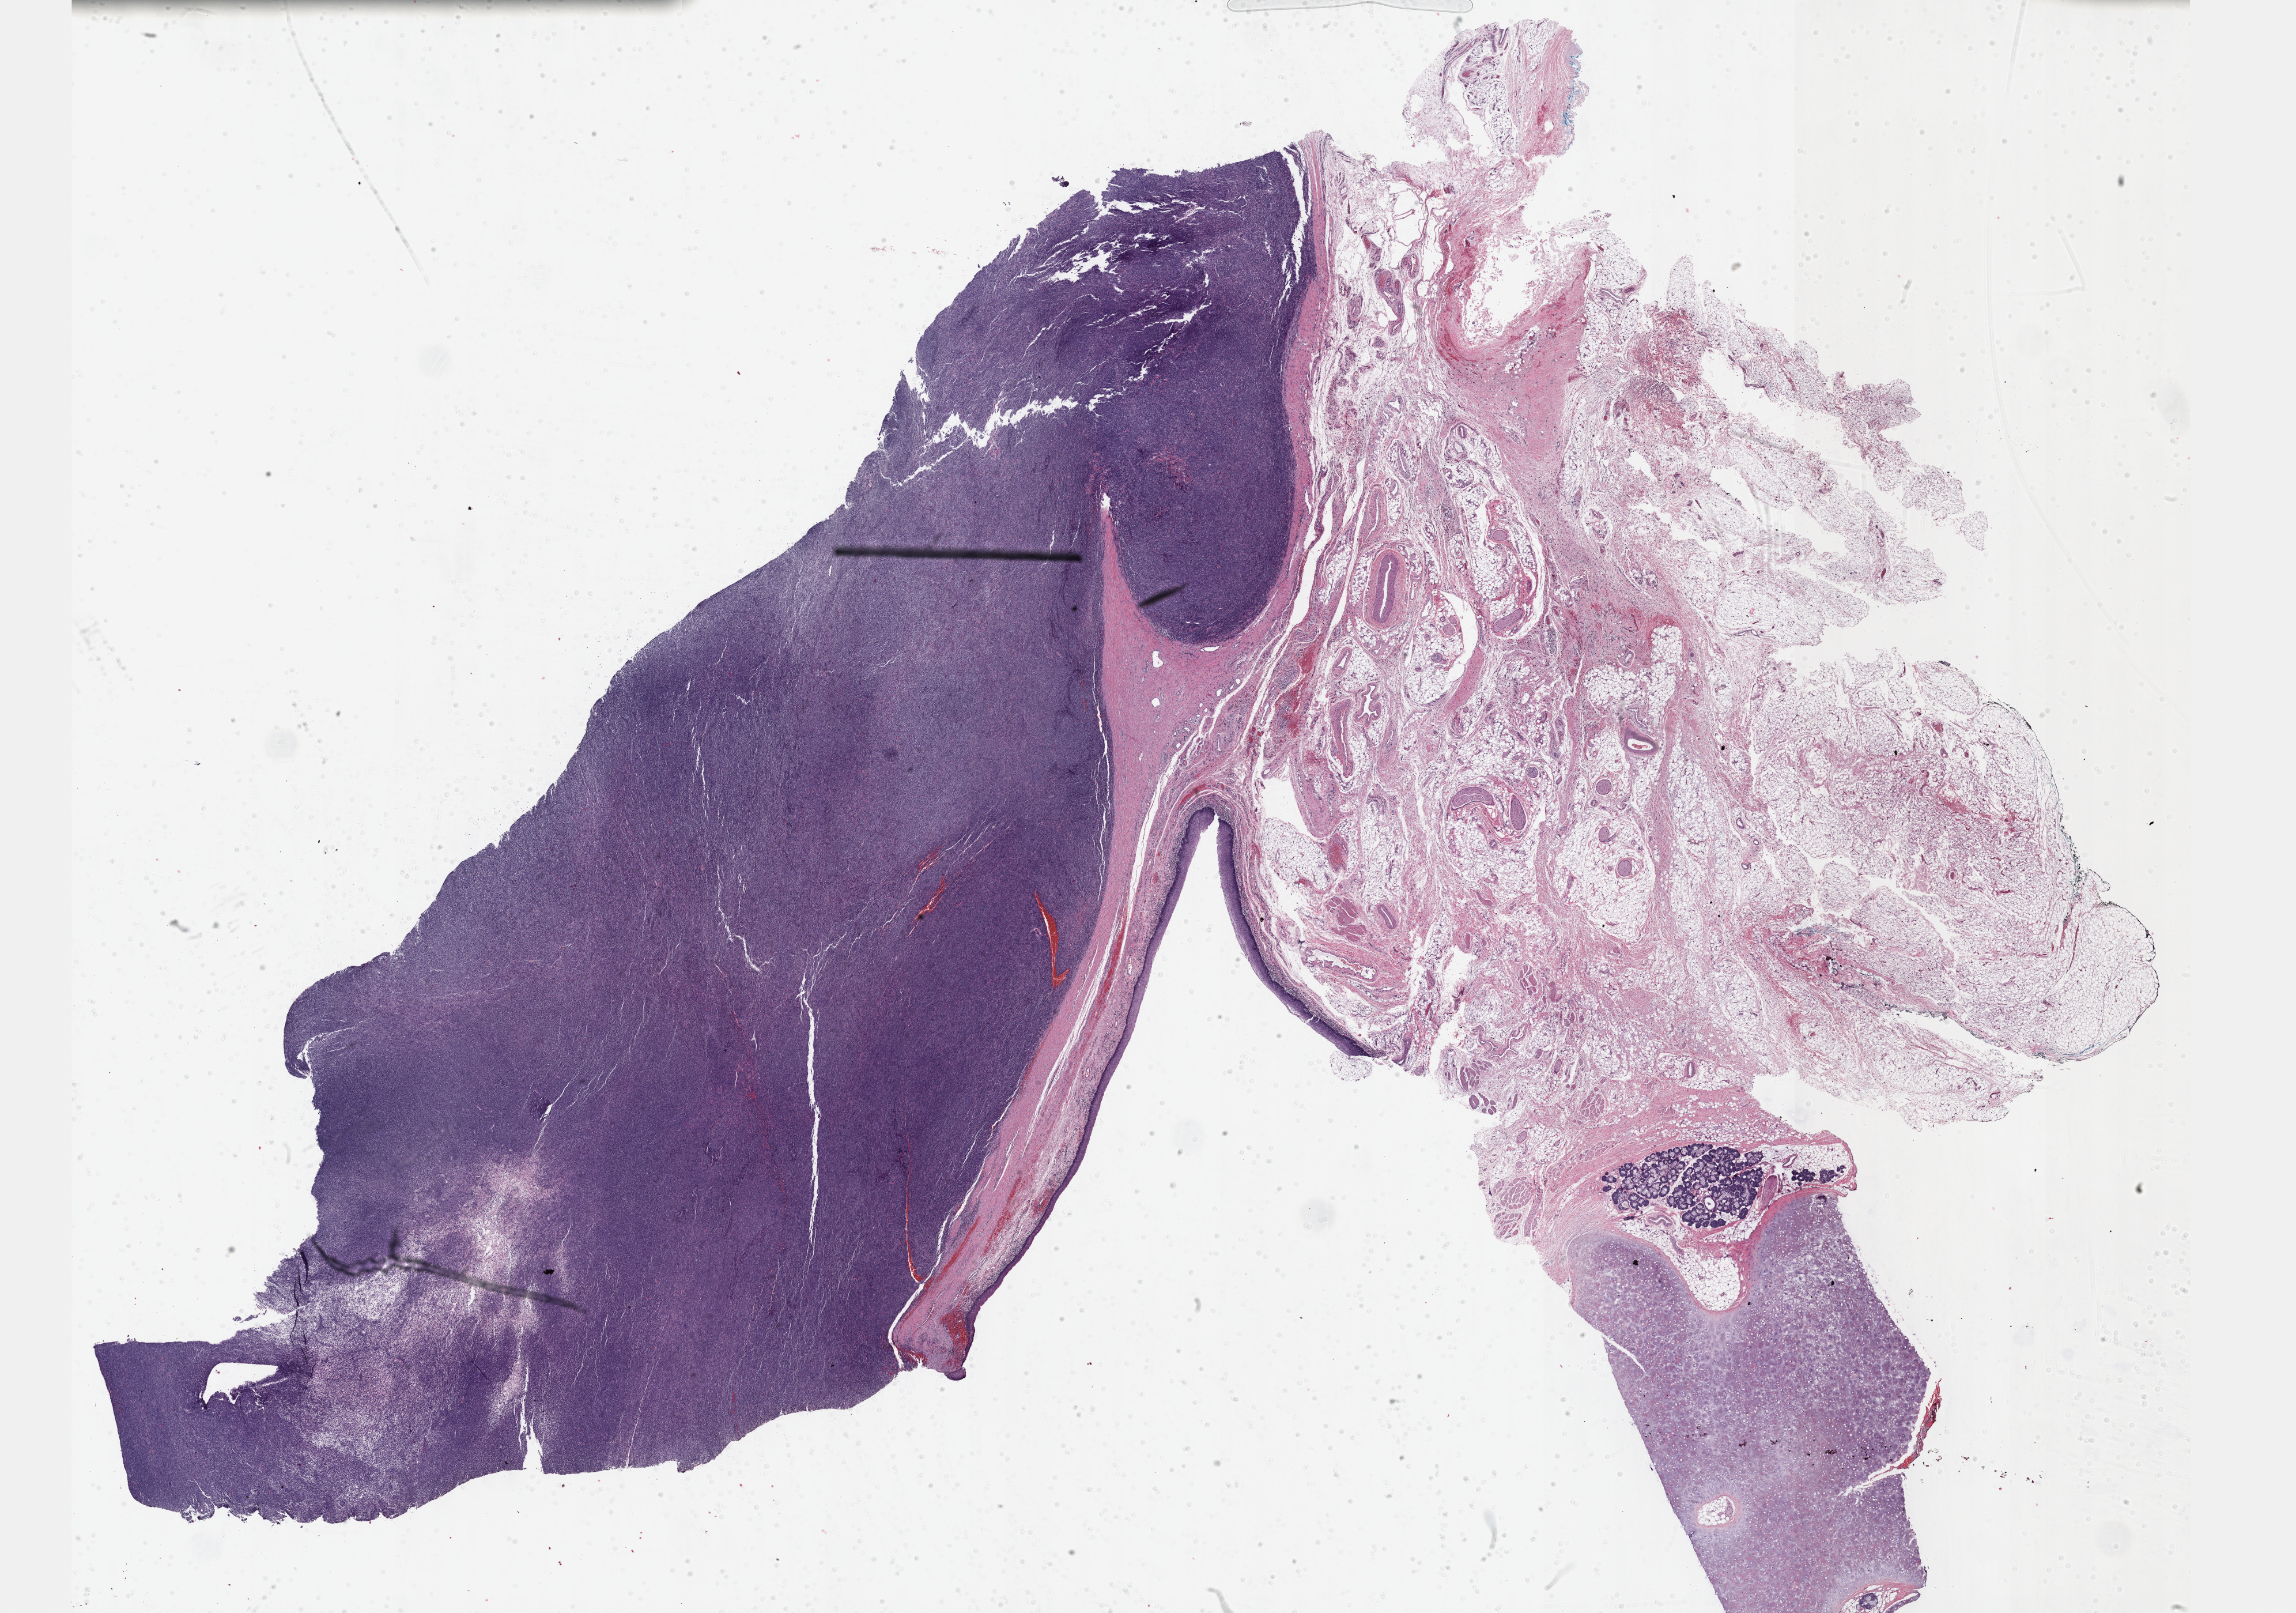
Digitized H&E tissue section (whole slide), whole scanned area (about 32.2 x 22.6 mm, slide scanned at 40x) shown as a low-resolution overview. Formalin-fixed paraffin-embedded (FFPE) diagnostic section. Sample: primary tumour, connective, subcutaneous and other soft tissues. Male patient; age at initial diagnosis 28 years.
Pathologic diagnosis: Synovial sarcoma, spindle cell (connective, subcutaneous and other soft tissues of head, face, and neck).